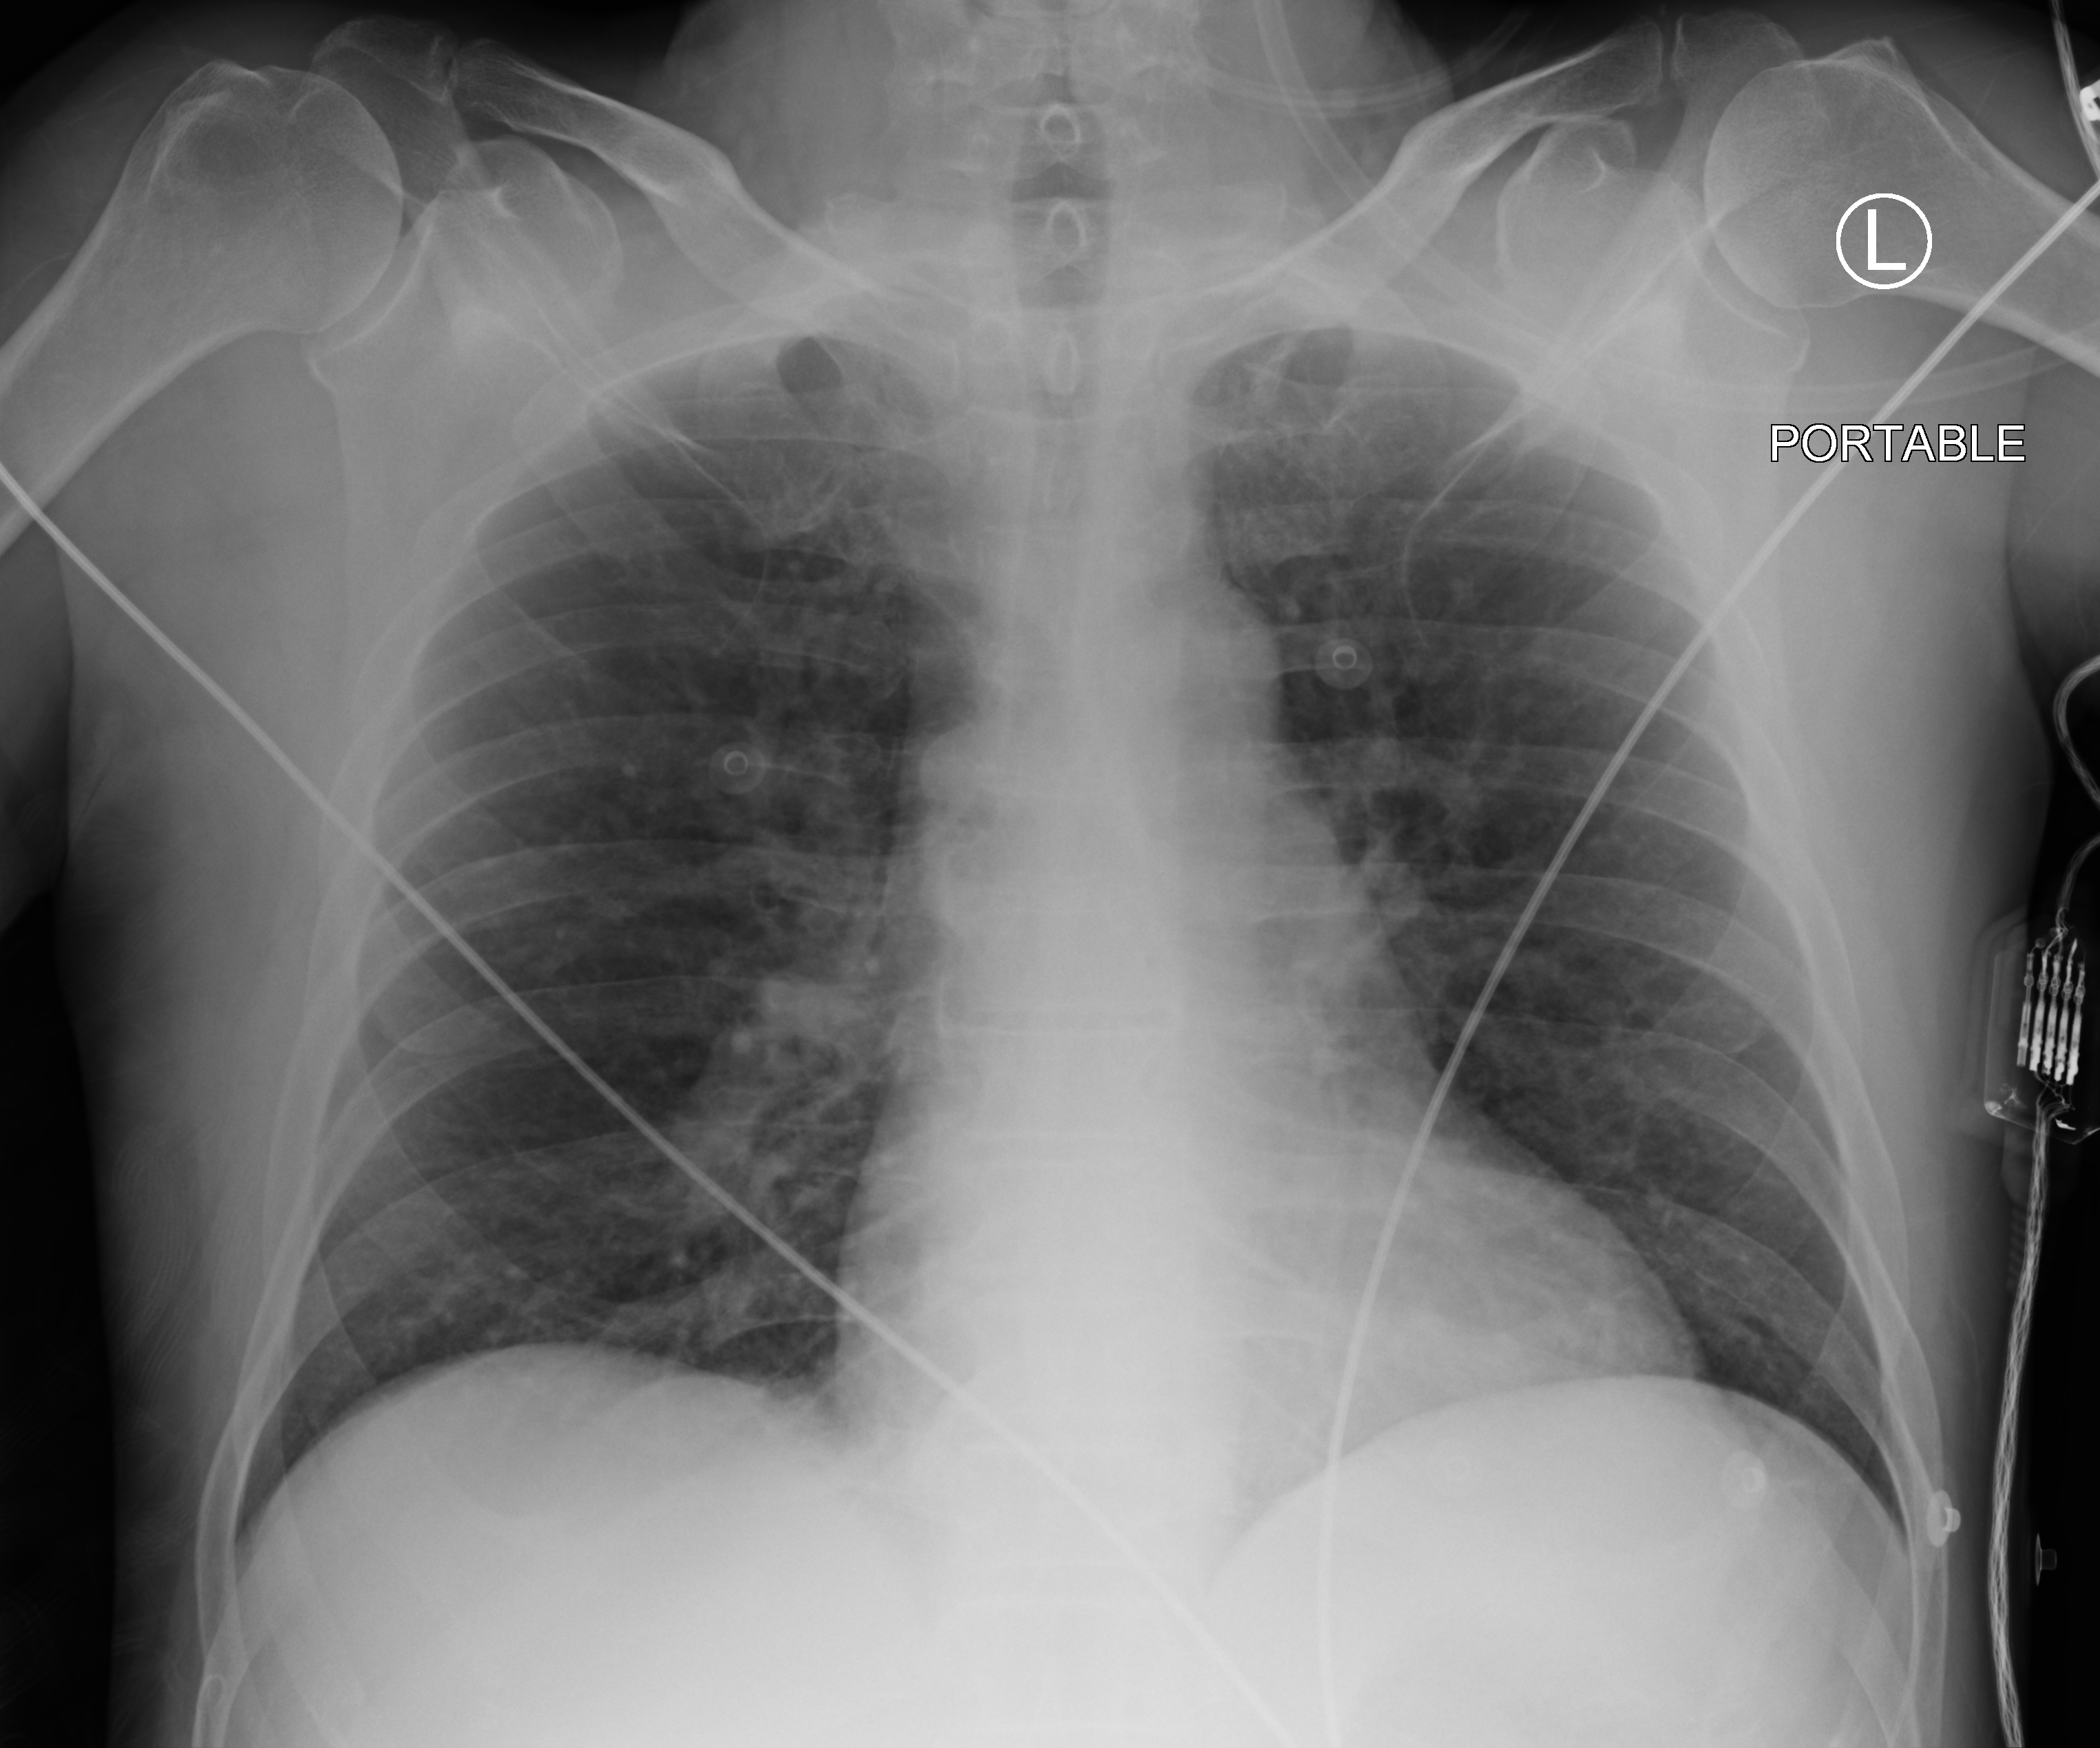
Bedside chest radiograph (computed radiography); anteroposterior (AP) projection. Patient hospitalised with COVID-19; male, aged 18–59 years.
From the hospital-stay record, not from the radiograph (when in the stay this image was taken is not recorded): mechanically ventilated during this hospital stay: no; admitted to intensive care during this hospital stay: no.